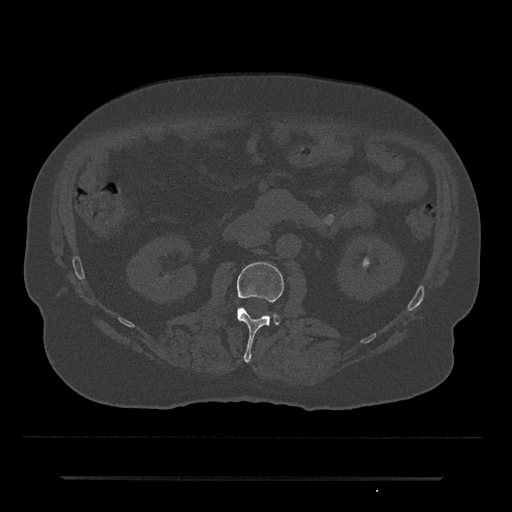
CT including the spine, one axial slice. Position 2 of 797 along the scan axis. 120 kVp. Bone window (W 1800 / L 400 HU). 512 × 512 image matrix, field of view 437 × 437 mm. Male patient, age 69 years. From the clinical record (not read from this slice): primary cancer: prostate.
Outlined on this slice (semi-automatically segmented with operator editing):
- L2 vertebra: bounding box [x1, y1, x2, y2] px = [237, 262, 284, 362]